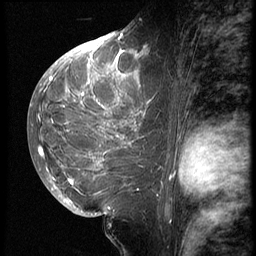
Breast MRI (dynamic contrast-enhanced), one sagittal slice; position 31 of 62 along the scan axis; 3 images stored at this slice position (order not interpretable as contrast timing); 1.5 T; TE 4.2 ms, TR 9 ms; 2.5 mm slice thickness; 256 × 256 image matrix, field of view 180 × 180 mm. Patient: female, 28 years. From the clinical record (not read from this slice): setting: breast cancer imaged before/during neoadjuvant chemotherapy.
Outlined on this slice (semi-automatically segmented with operator editing):
- analysis volume of interest (the breast-tissue region the enhancement analysis was run in; not a lesion): bounding box [x1, y1, x2, y2] px = [42, 45, 163, 207]
- tumour enhancement mask (voxels above the 140 % enhancement threshold inside the analysis volume of interest): [42, 45, 146, 185]